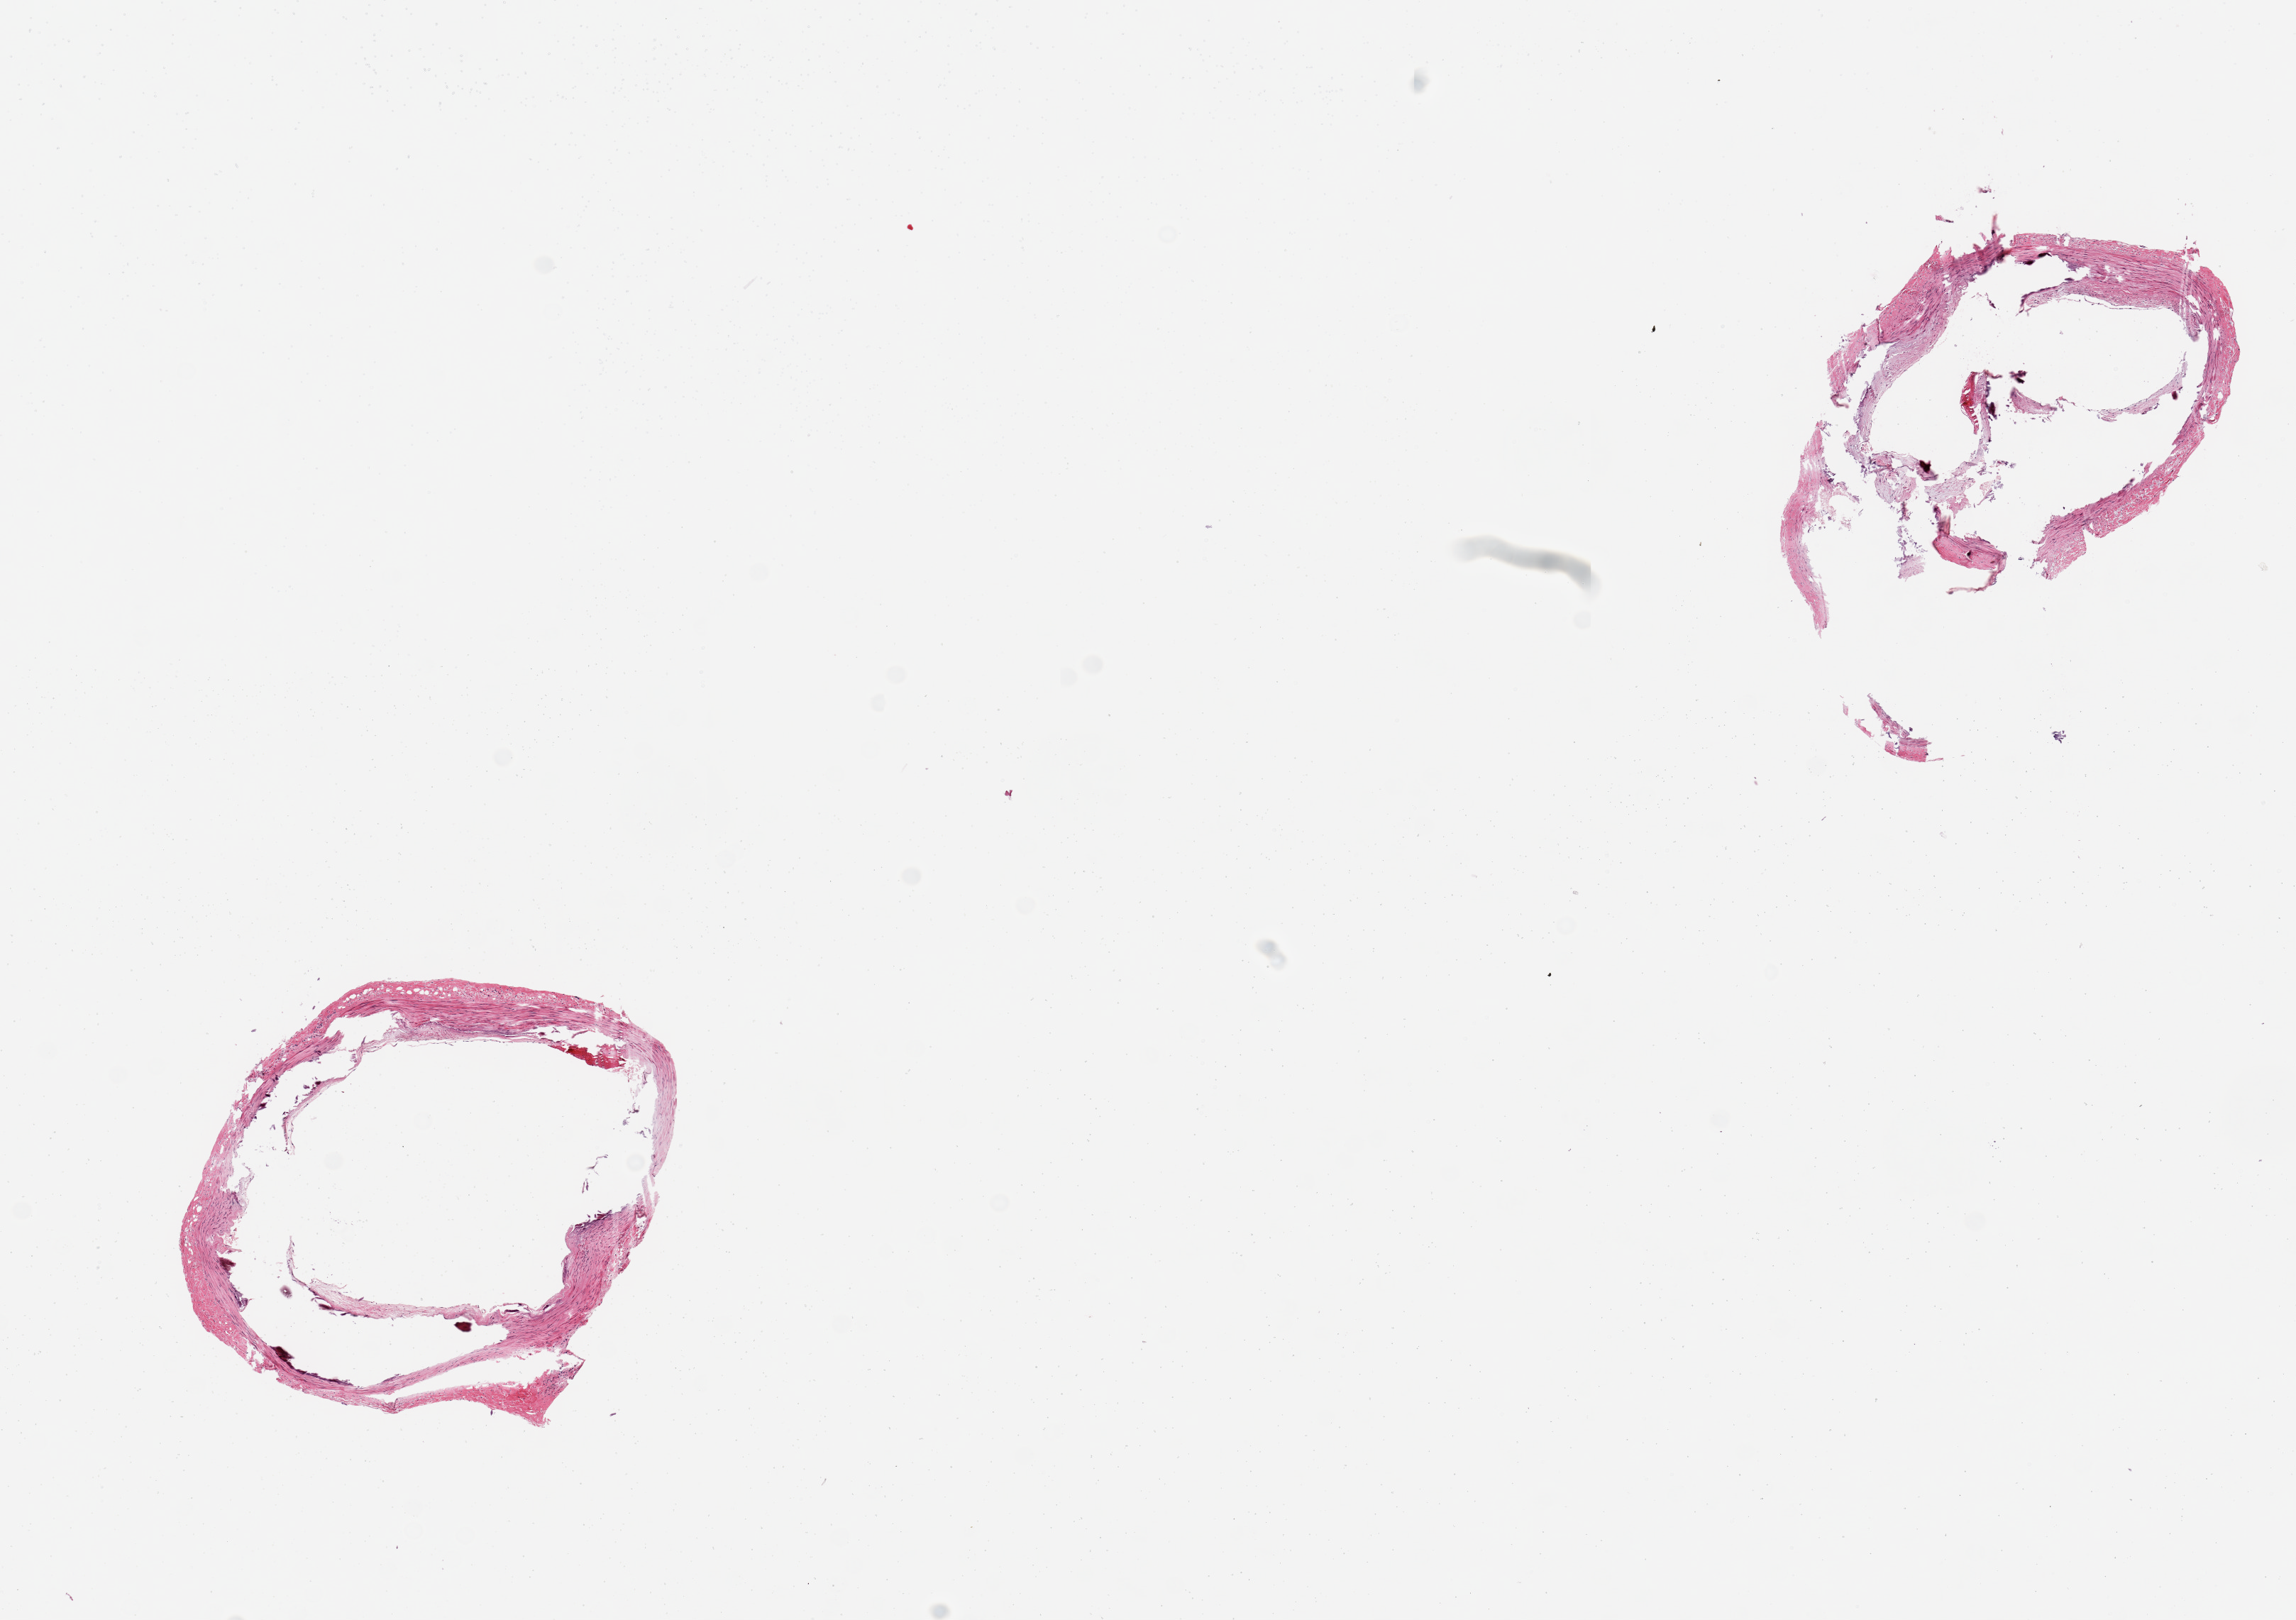
H&E whole-slide image, low-resolution overview of the scanned area, about 12.8 x 9.0 mm; PAXgene-fixed paraffin-embedded (PFPE) section; section of tibial artery (target tissue); donor tissue sample. Male donor.
Pathologist's review note for this sample: 2 pieces; heavily calcified; small amount of residual arterial wall present.